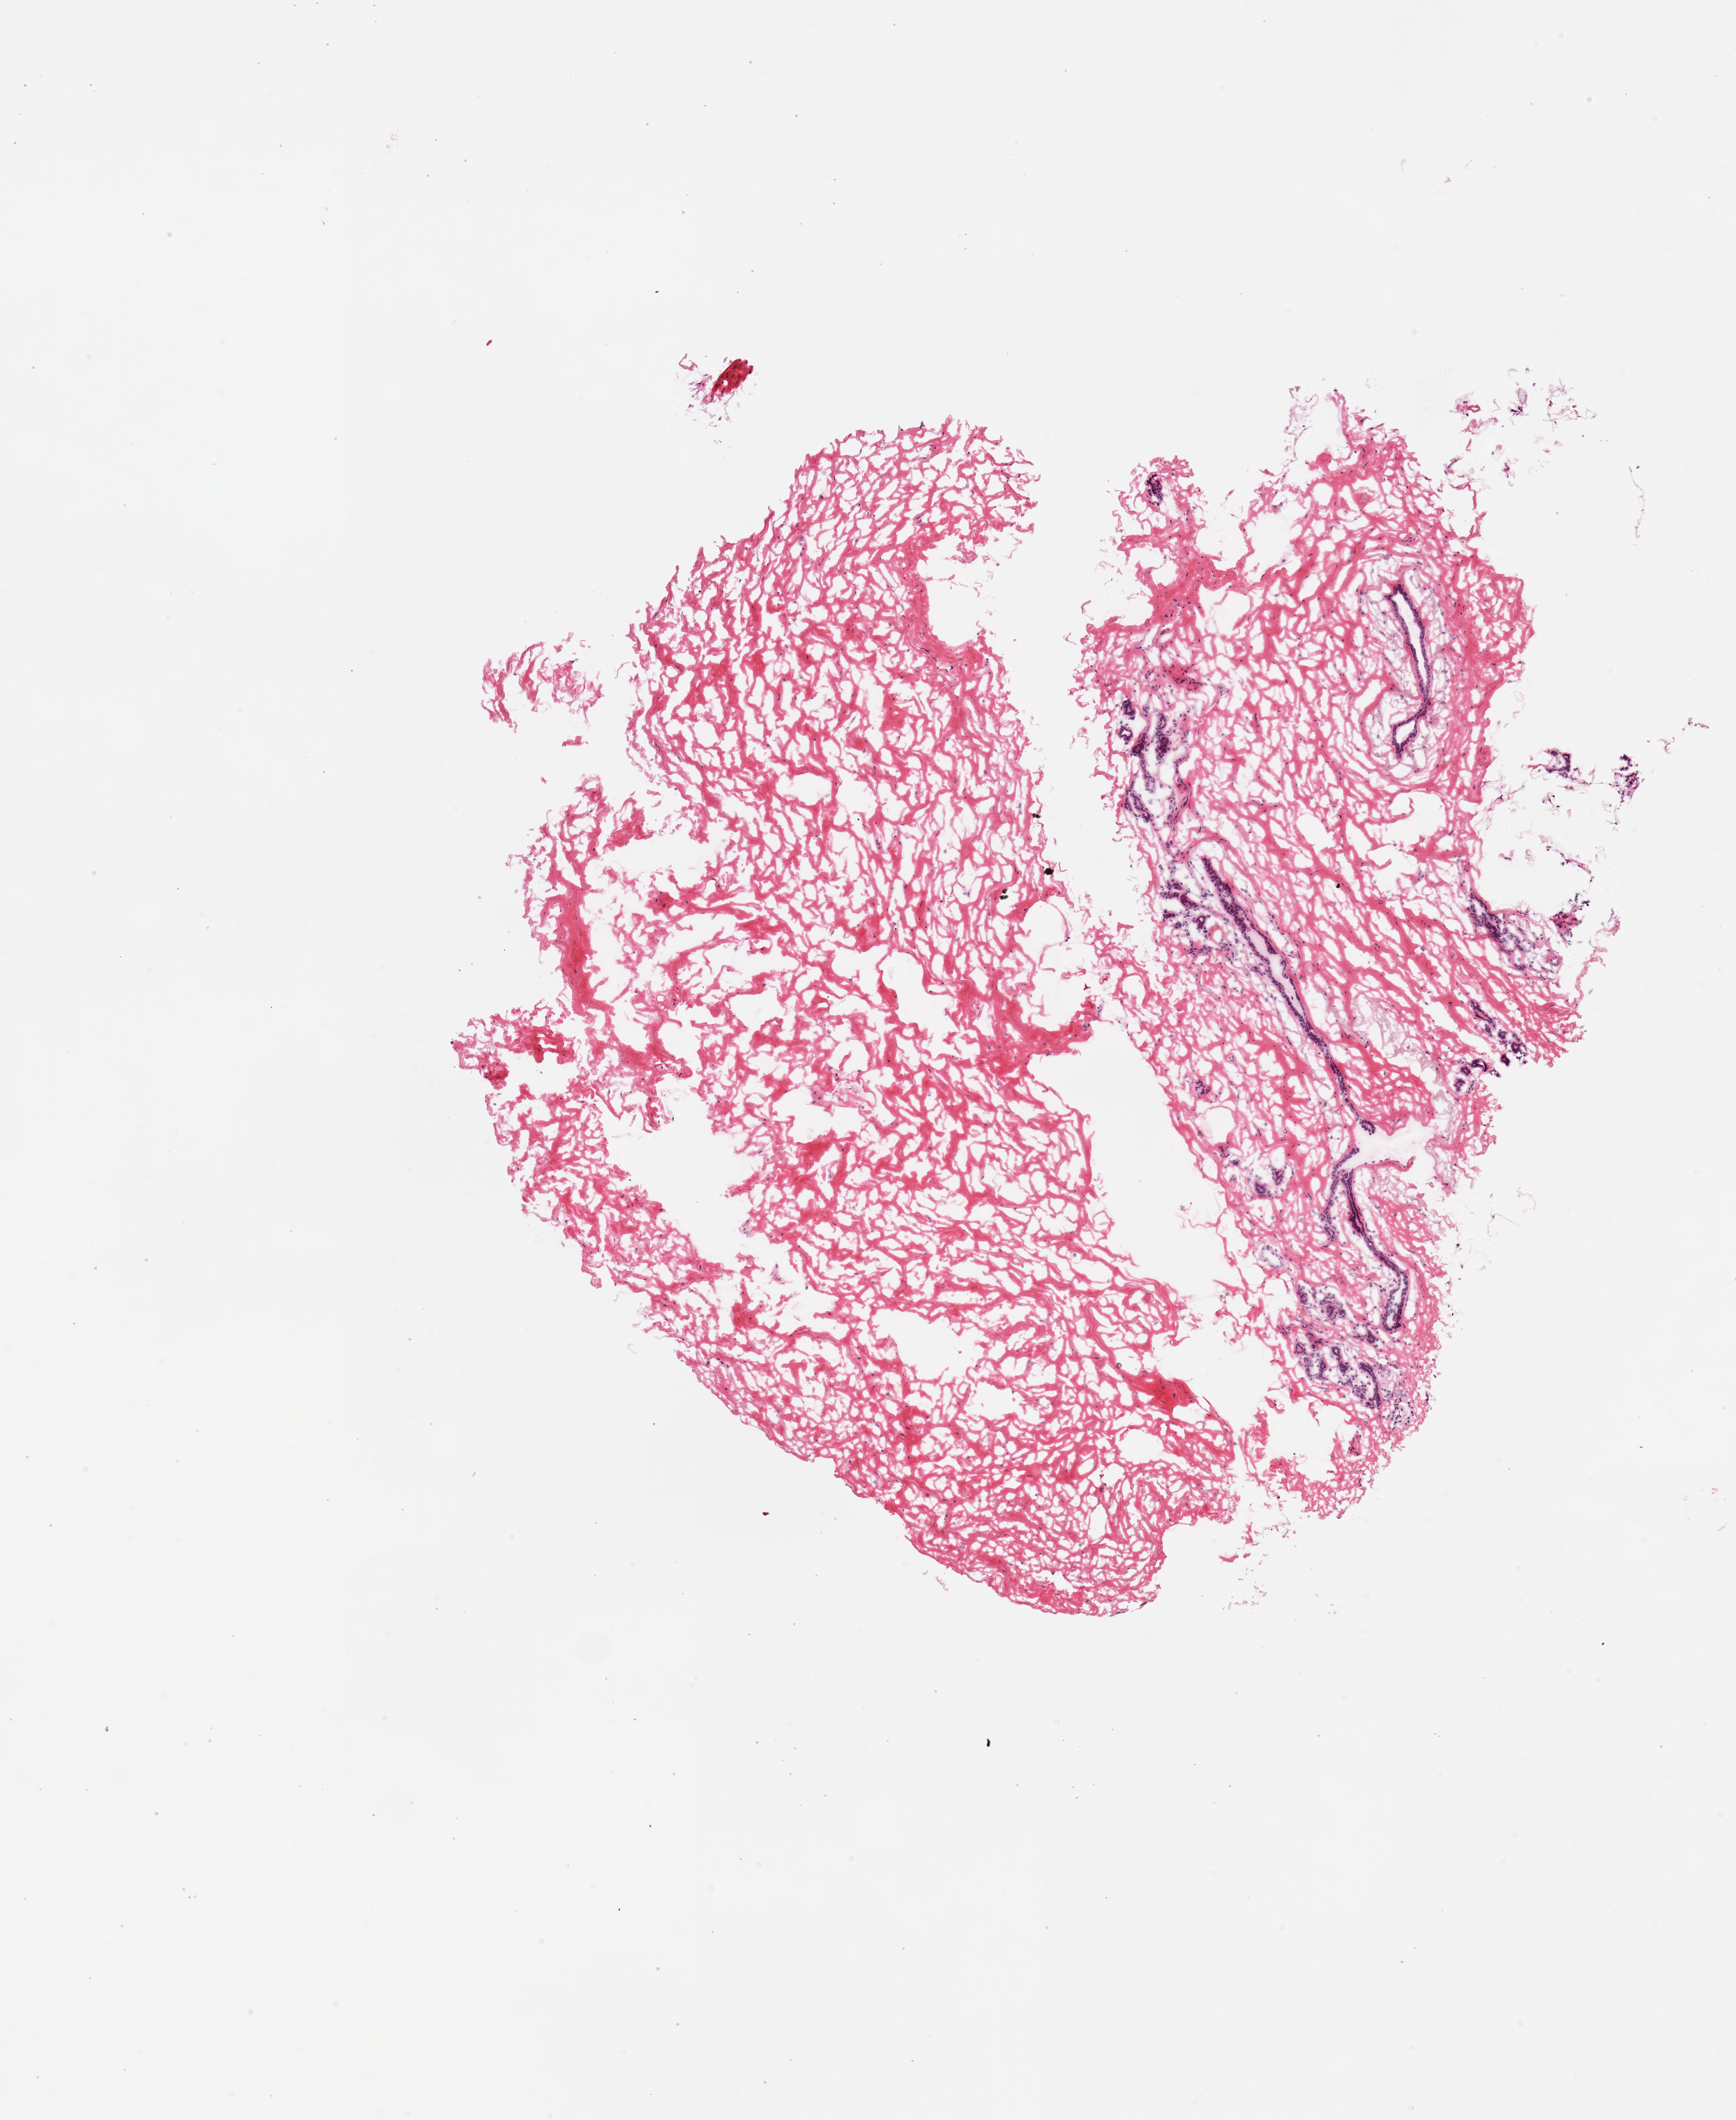
Whole-slide image, haematoxylin and eosin stain — whole scanned area (about 4.9 x 6.0 mm, slide scanned at 20x) shown as a low-resolution overview, frozen section (dry ice), section of breast (target tissue), tissue donor sample. Female donor.
Review note (as recorded): 1 piece, stroma, ductal/lobular elements.